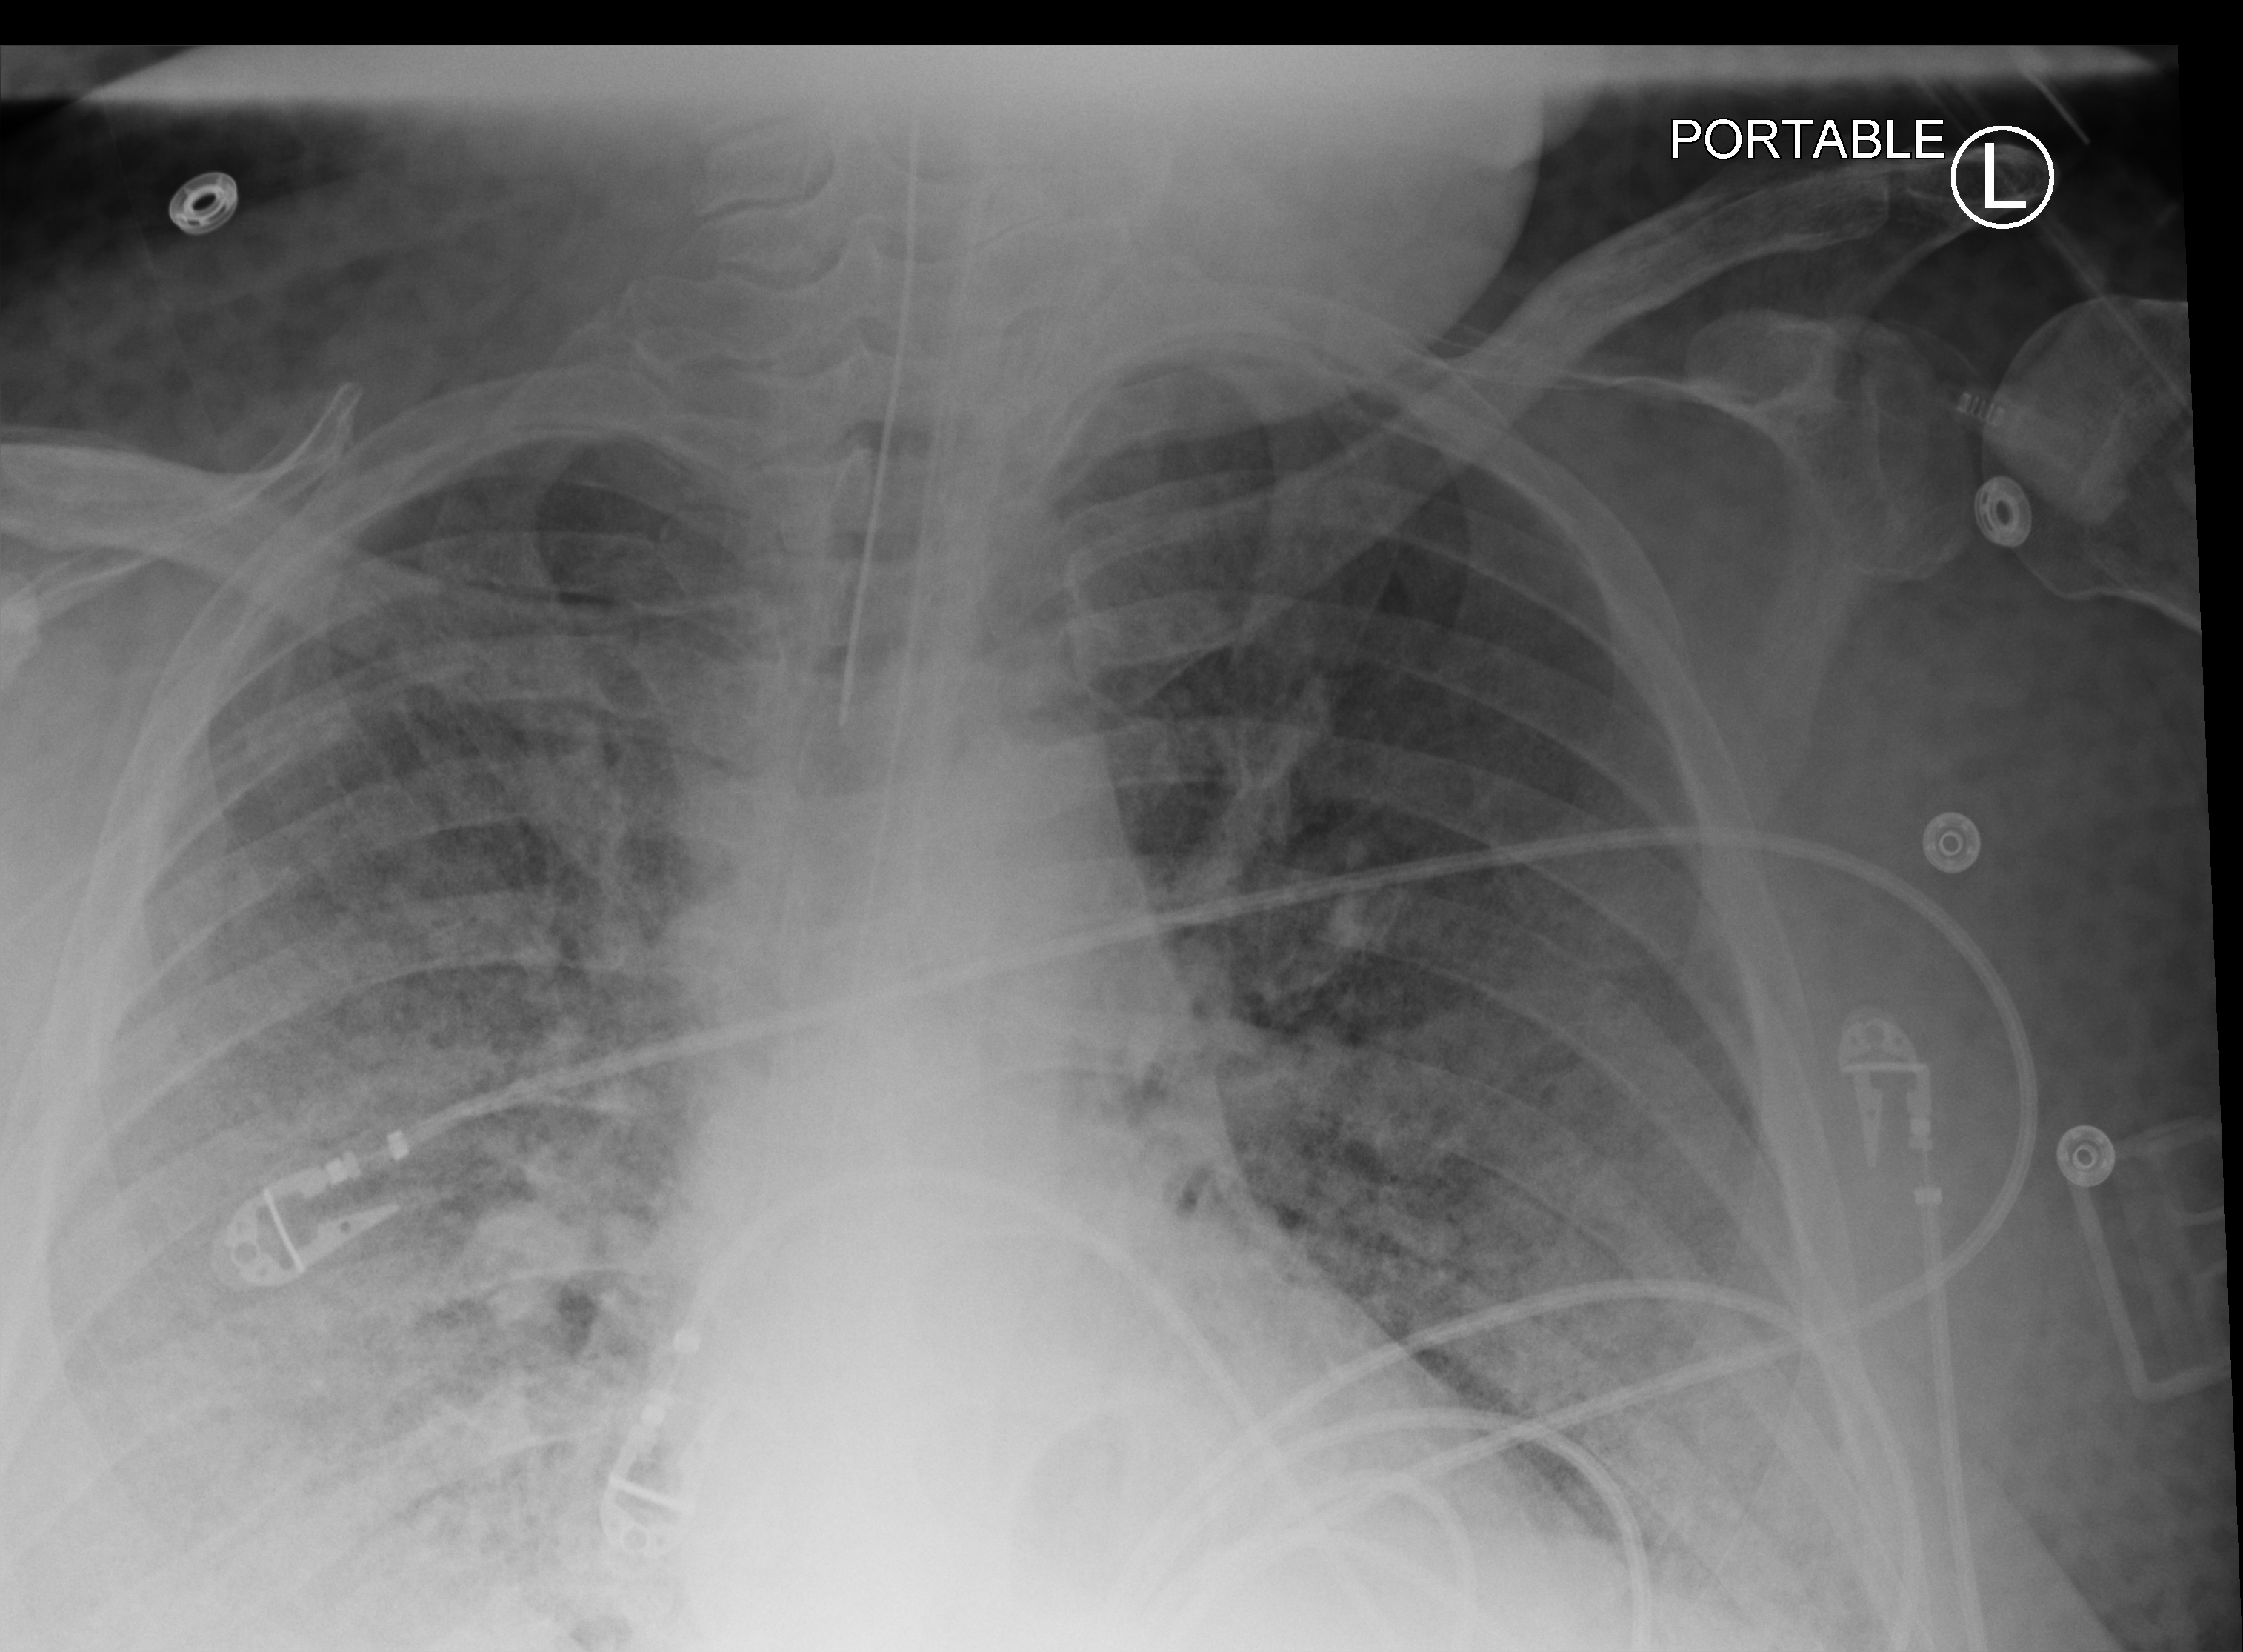
Chest X-ray (portable). Adult patient hospitalised with COVID-19, age 18–59 years.
From the hospital-stay record, not from the radiograph (when in the stay this image was taken is not recorded): admitted to intensive care during this hospital stay: yes.